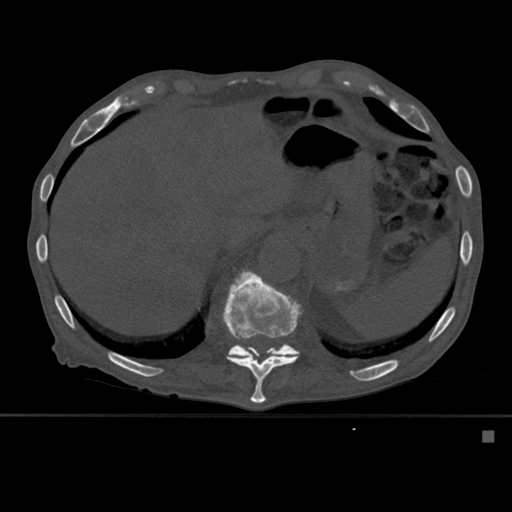
CT including the spine, one axial slice. Bone window (W 1800 / L 400 HU). 1.5 mm slice thickness. 512 × 512 image matrix. Patient: male, 78 years. From the clinical record (not read from this slice): primary cancer: prostate.
Annotated regions visible in this slice (semi-automatically segmented with operator editing):
- T11 vertebra: bounding box (x1, y1, x2, y2) in pixels: (222, 270, 301, 404)
- T12 vertebra: (227, 344, 300, 358)